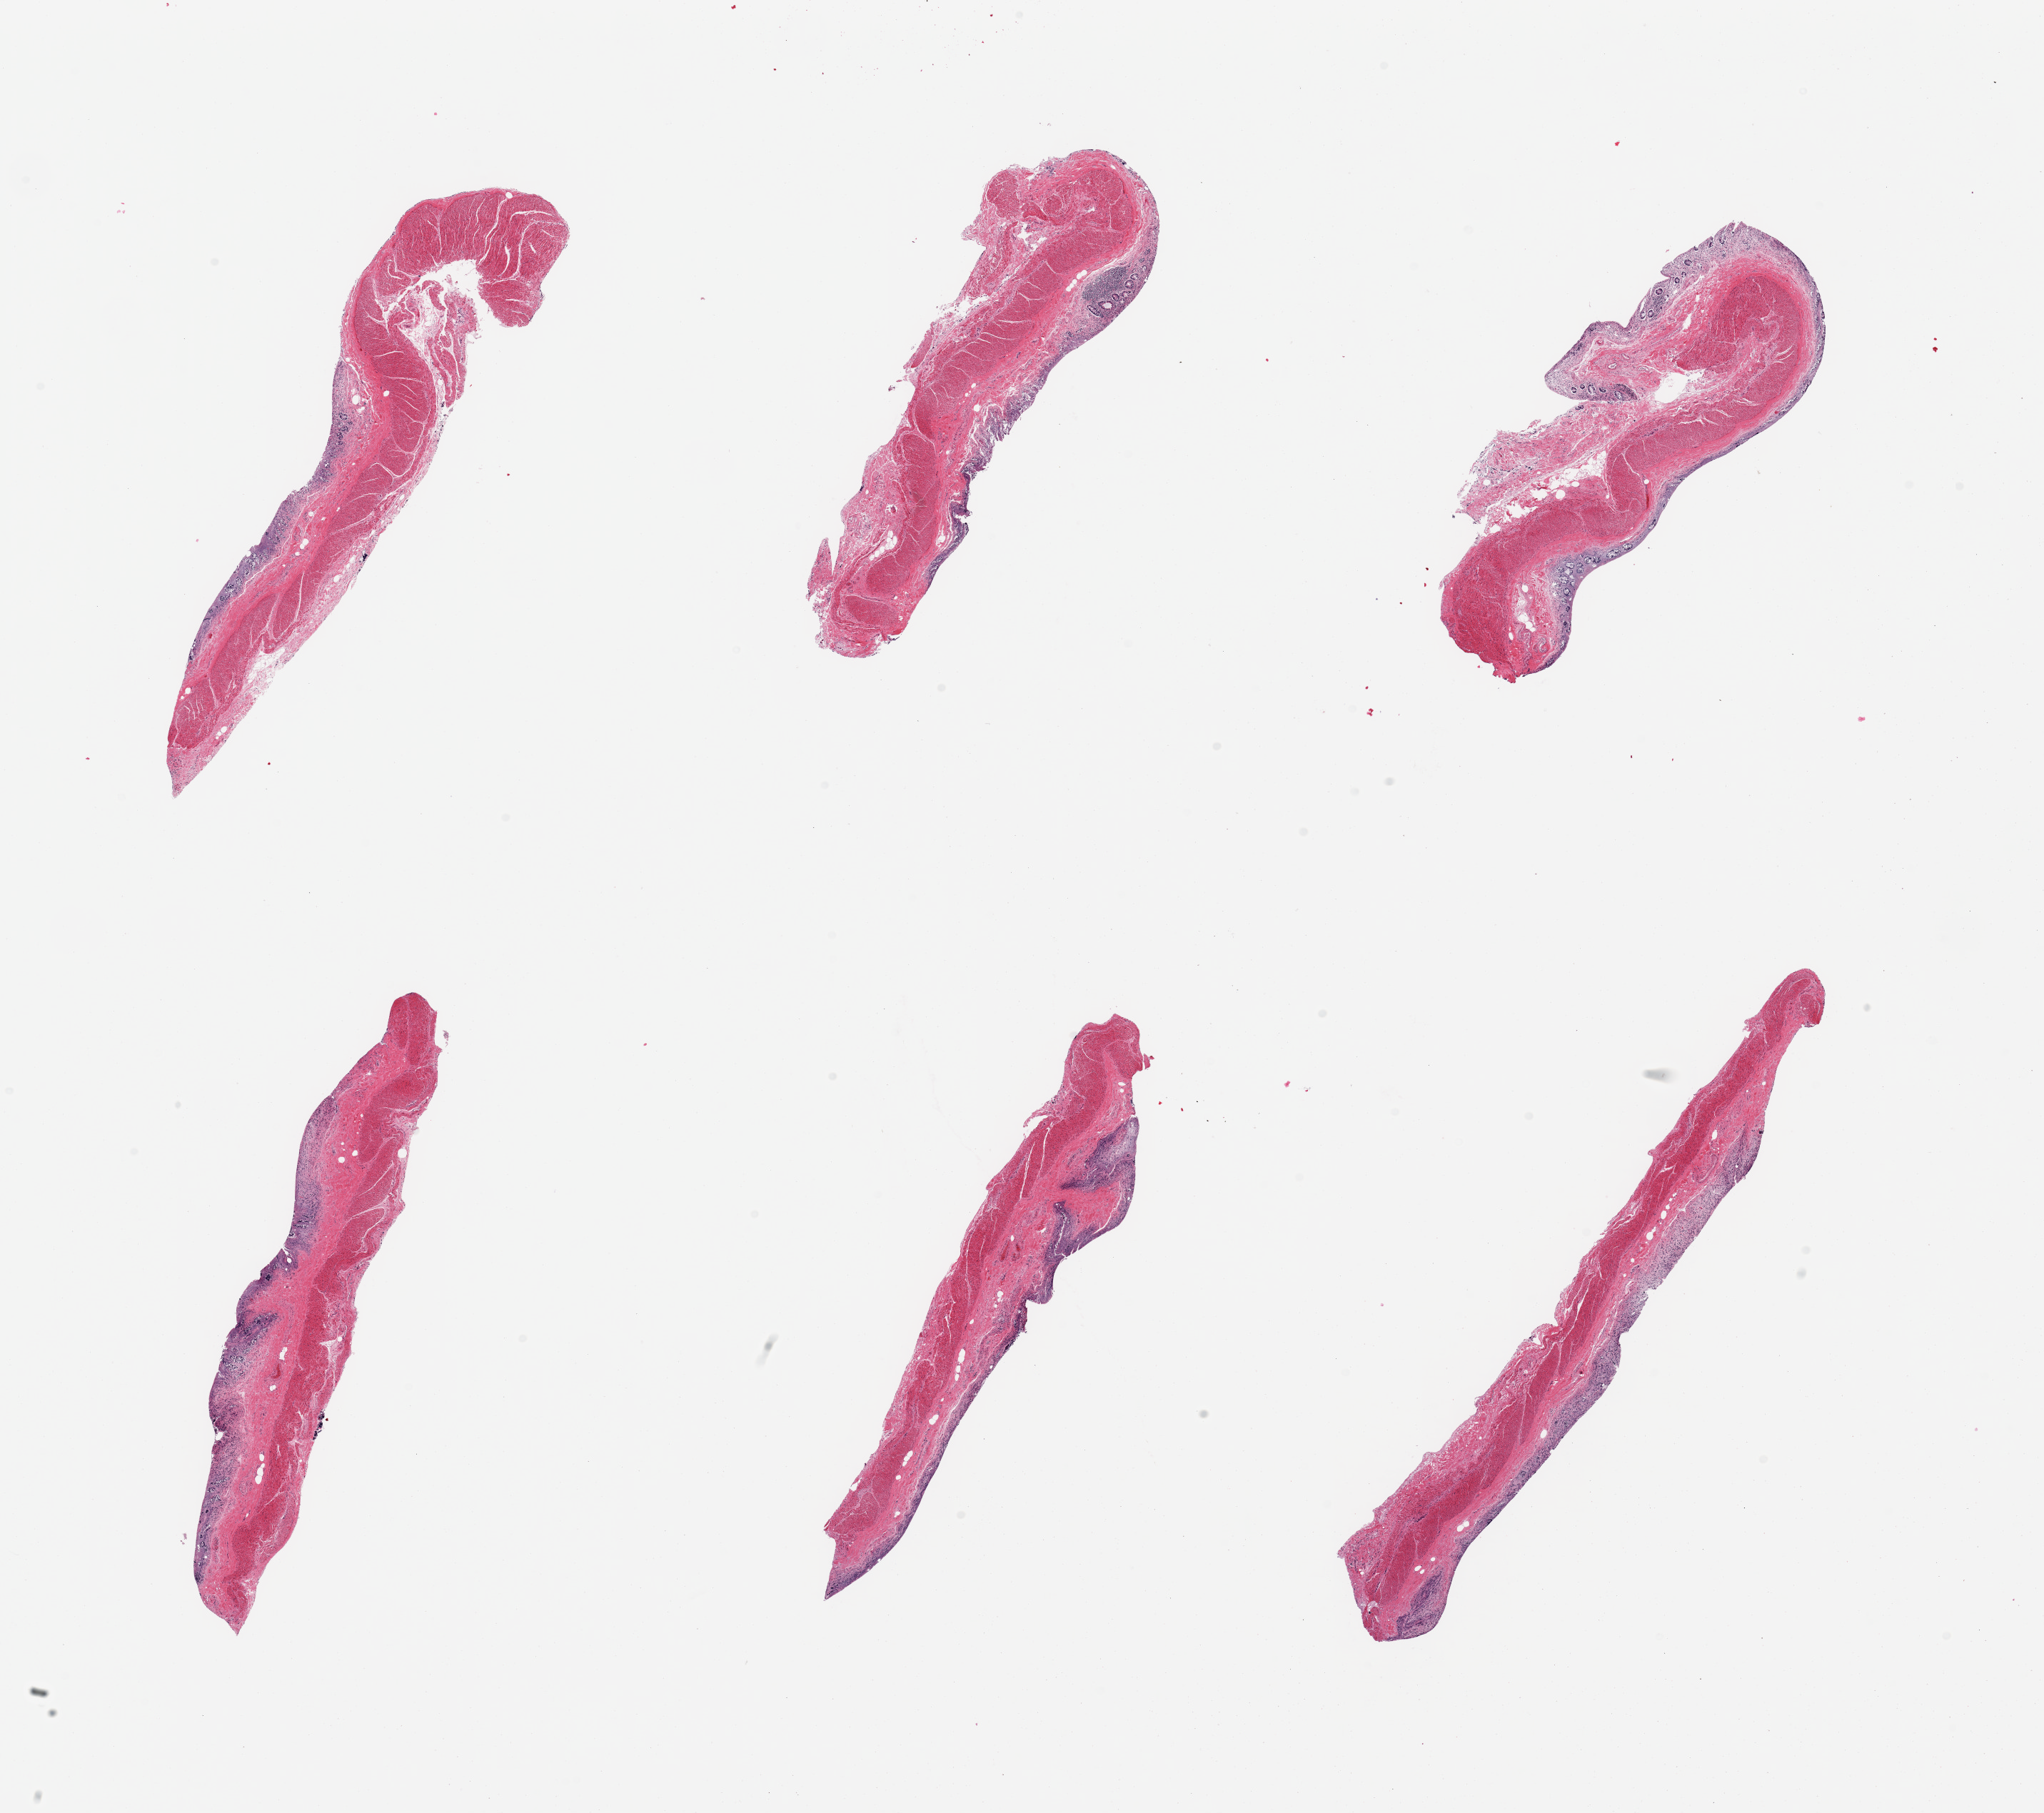
Whole-slide image, haematoxylin and eosin stain, shown as a low-resolution overview of the whole scanned area (about 22.6 x 20.1 mm), PAXgene-fixed, paraffin-embedded tissue, target tissue: transverse colon, tissue donor sample. Male donor.
Reviewer comment on this tissue sample: 6 pieces; severly autolyzed mucosa and preserved muscularis.